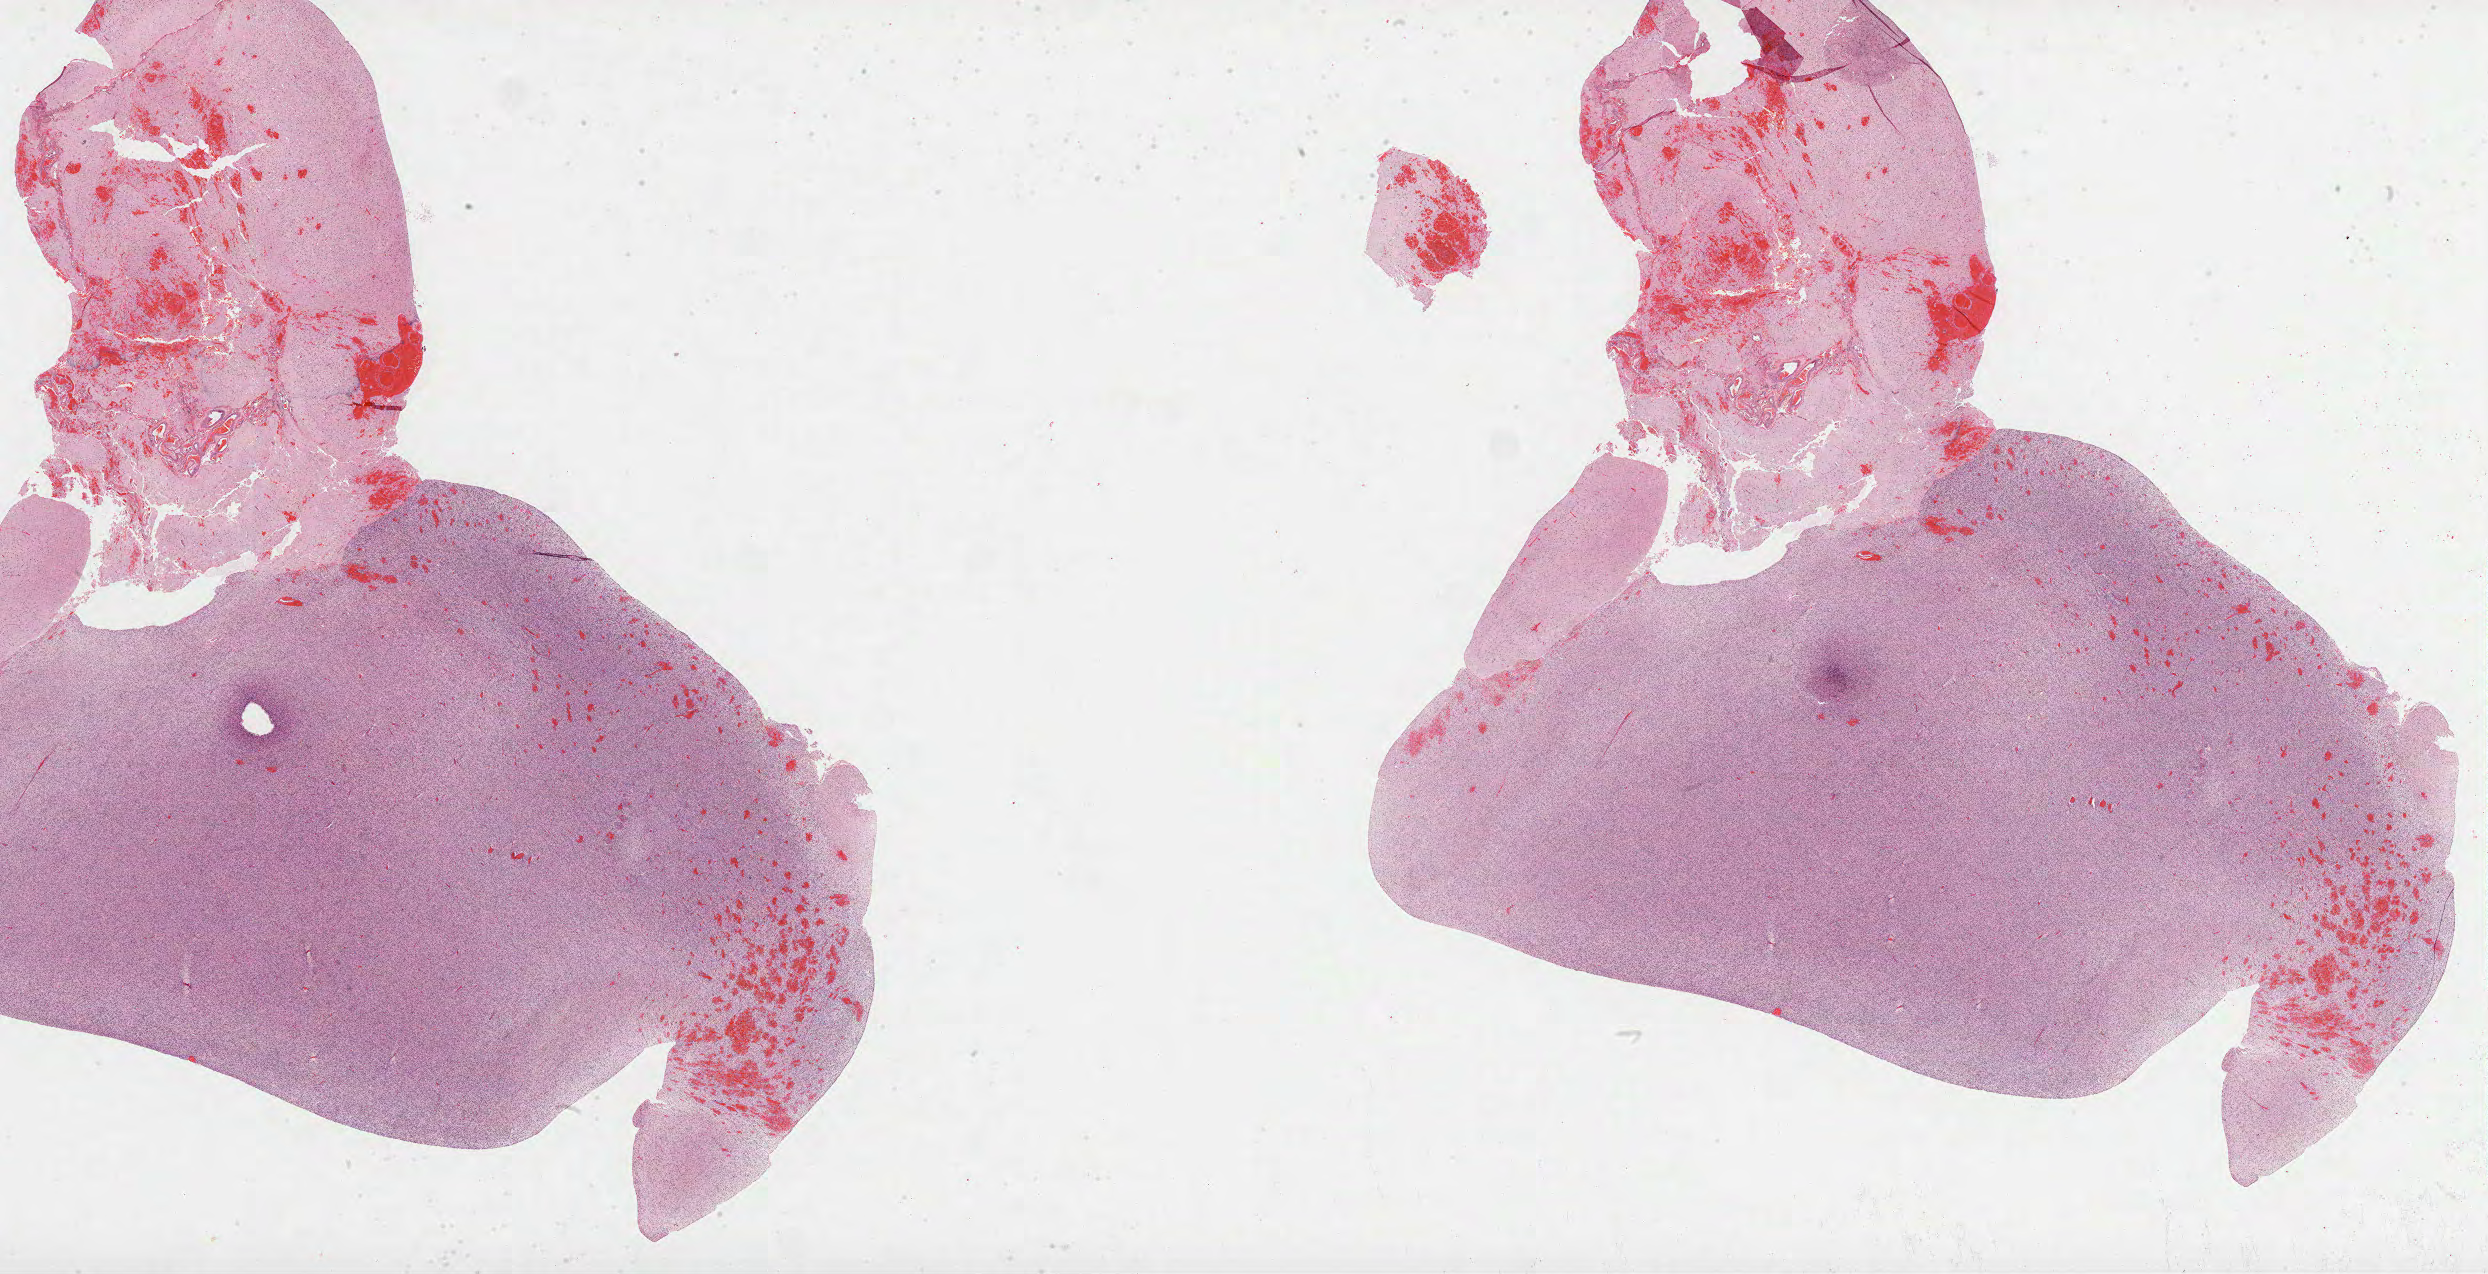
Whole-slide histology image, Hematoxylin and eosin (H&E) stained, whole scanned area (about 40.1 x 20.5 mm, from a 40x scan) shown as a low-resolution overview, FFPE section, brain, primary tumour sample. Female, age 76 years at initial diagnosis.
- diagnosis: Glioblastoma